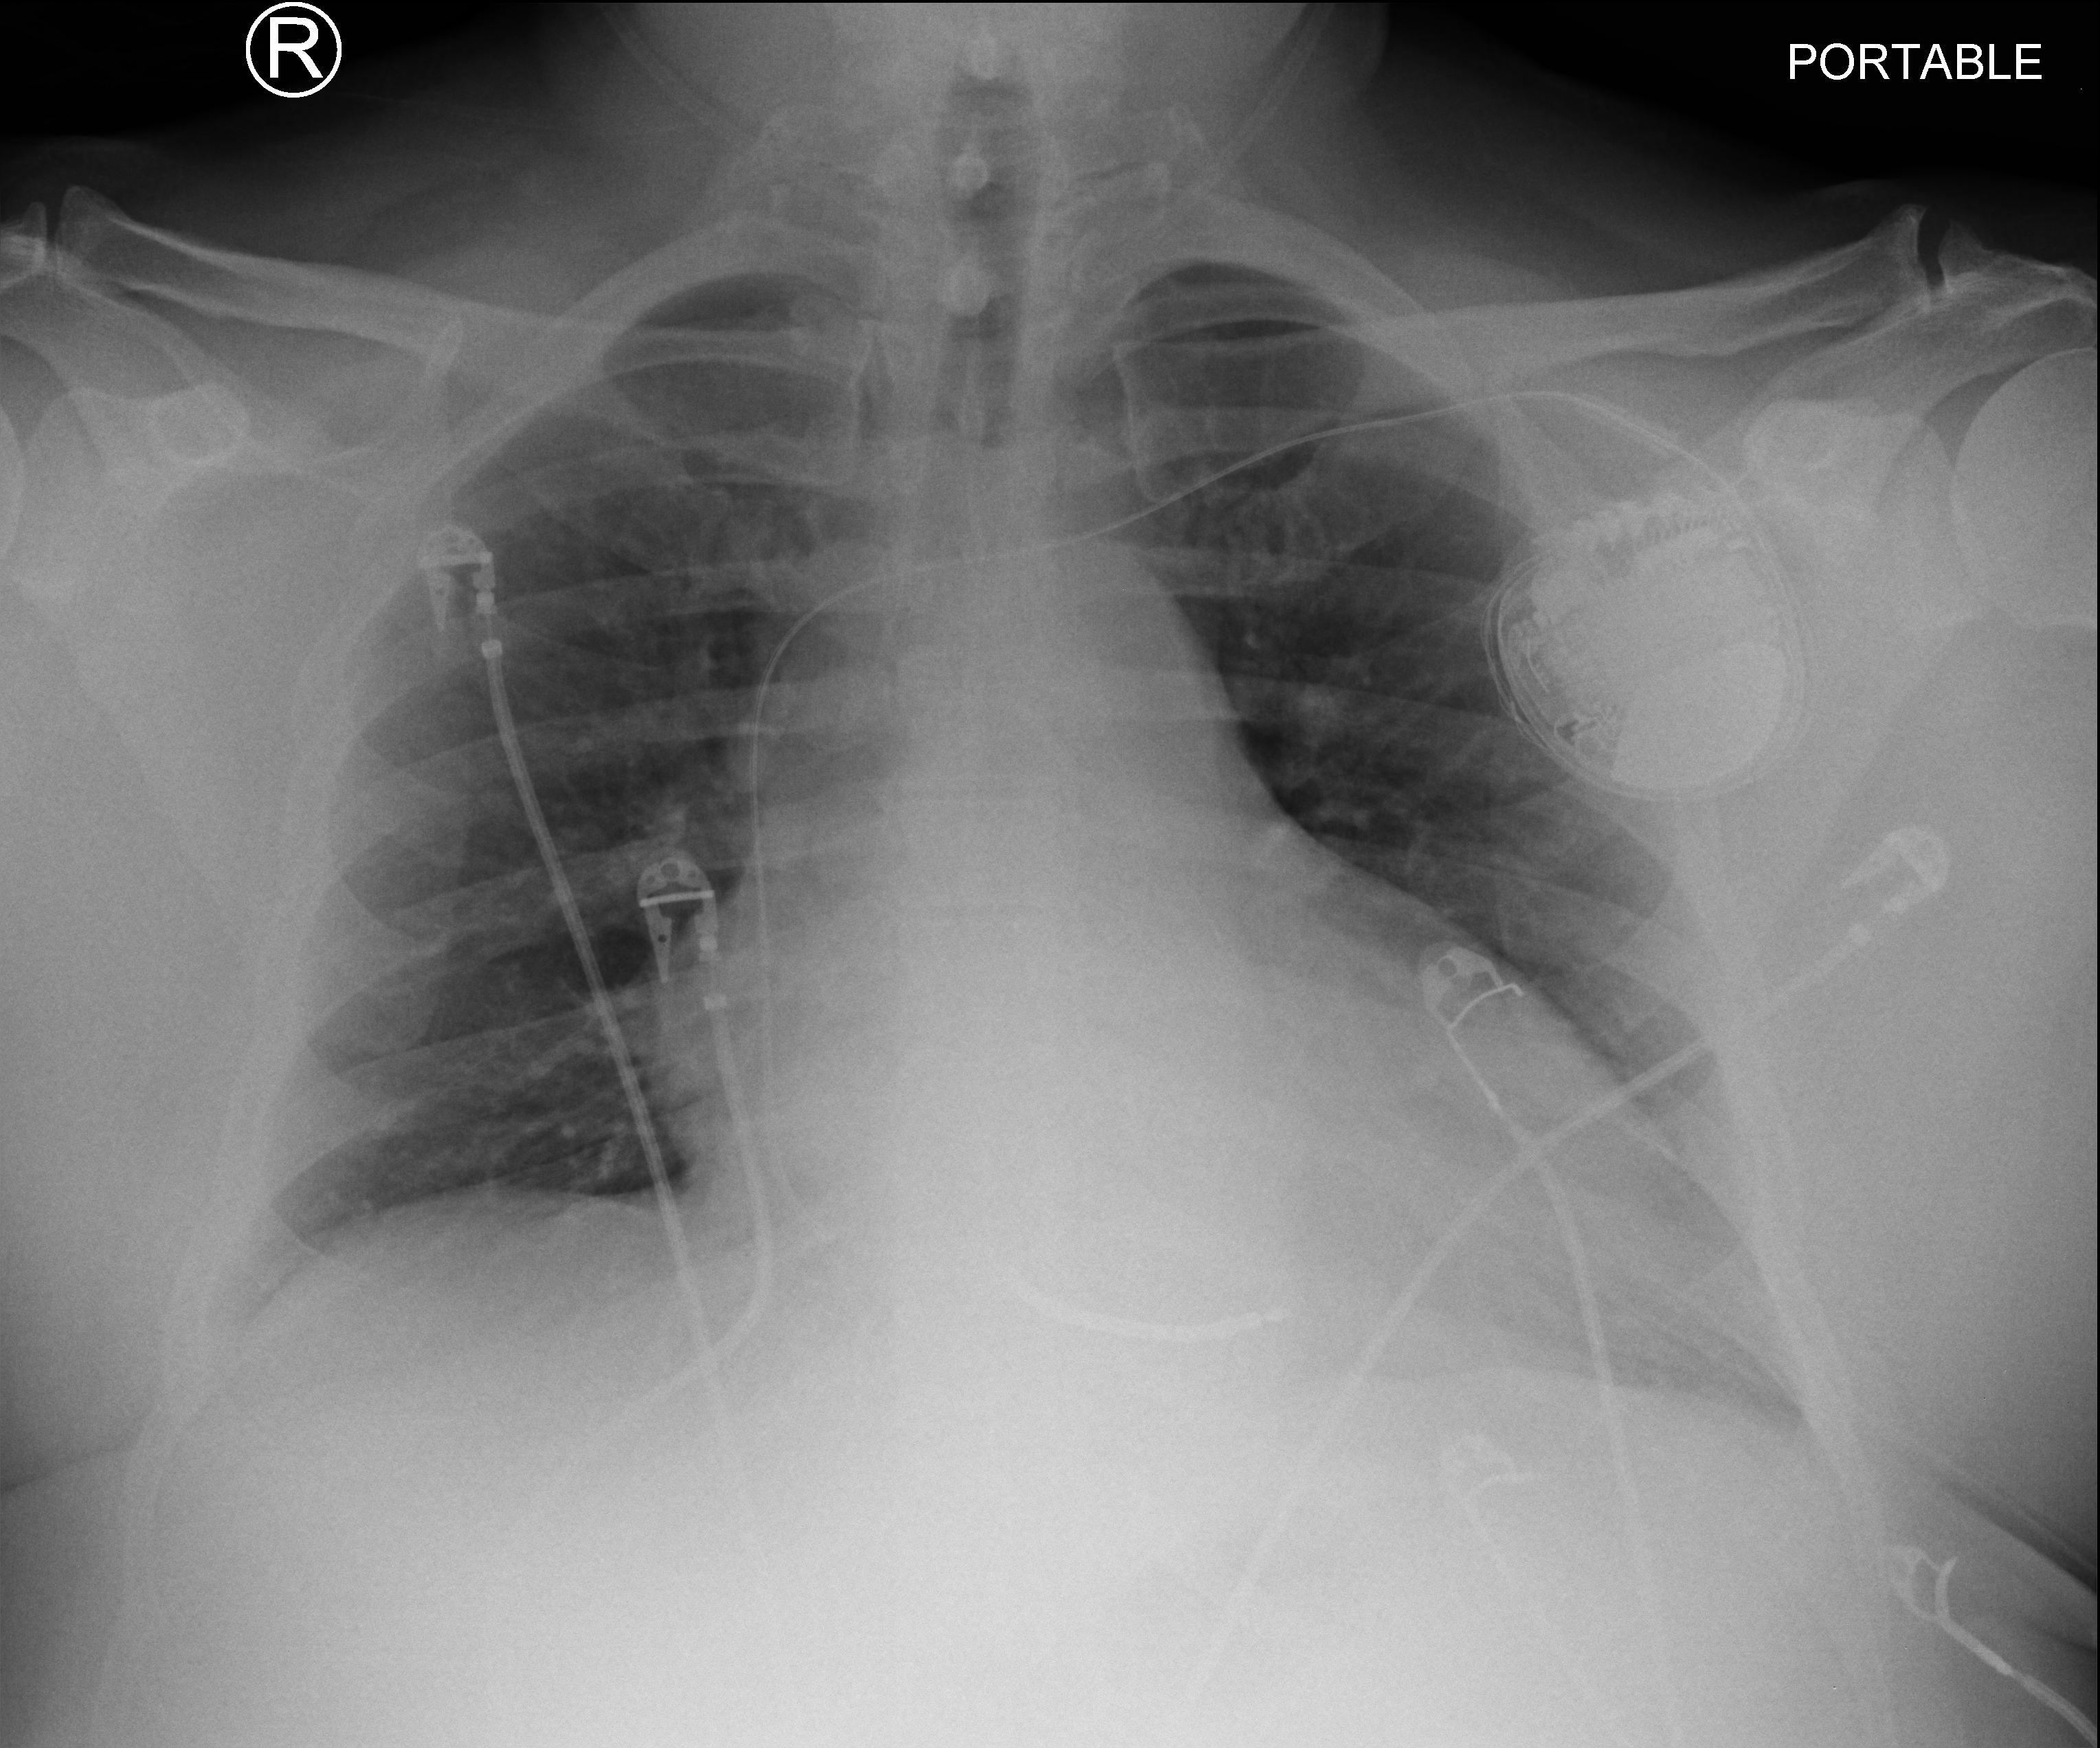
Bedside chest radiograph (computed radiography). Male patient hospitalised with COVID-19, age 18–59 years.
Admission-level facts for this patient (not findings on this image; timing relative to this image not recorded):
- other chronic lung disease (admission record): yes
- mechanically ventilated during this hospital stay: no
- hypertension (admission record): yes